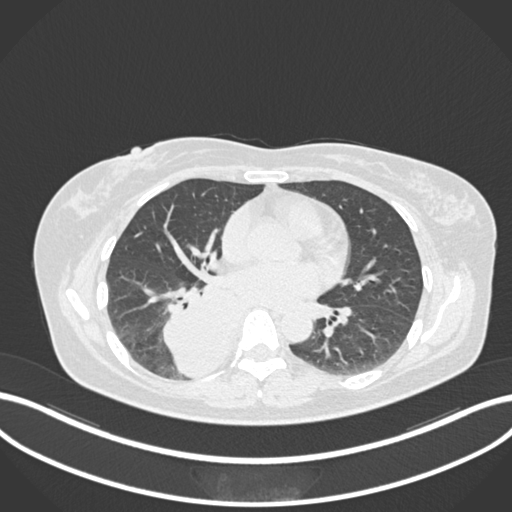
Chest CT, one axial slice. Position 580 of 677 along the scan axis. 120 kVp. Lung window (W 1500 / L -600 HU). 1 mm slice thickness. 512 × 512 image matrix, field of view 400 × 400 mm. Patient: female, 54 years. Case-level facts recorded for this patient, not image findings: clinical TNM (as recorded): T4 N0 M0.
Outlined on this slice (bounding box drawn by a radiologist):
- lung tumour (recorded histology: adenocarcinoma): bounding box [x1, y1, x2, y2] px = [158, 267, 243, 382]